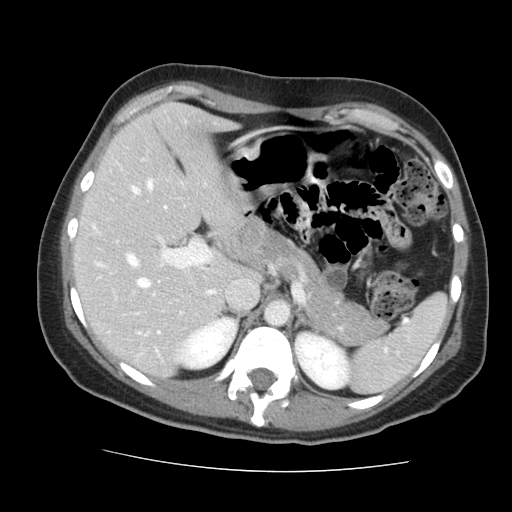
Contrast-enhanced abdominal CT, one axial slice. Position 96 of 144 along the scan axis. Intravenous contrast given. Soft-tissue window (W 400 / L 40 HU). 2.5 mm slice thickness. 512 × 512 image matrix. Female patient, age 46 years. Case-level facts recorded for this patient, not image findings: diagnosis: colorectal cancer liver metastases, imaged before liver resection; multiple liver metastases: no; largest metastasis: 2.8 cm; chemotherapy before resection: yes.
Outlined on this slice (outlined manually by an expert reader):
- hepatic veins: bounding box [x1, y1, x2, y2] px = [131, 180, 214, 294]
- liver: [76, 105, 242, 375]
- planned liver remnant (the part of the liver to remain after resection): [76, 105, 242, 375]
- portal vein (with intrahepatic branches): [127, 237, 213, 334]